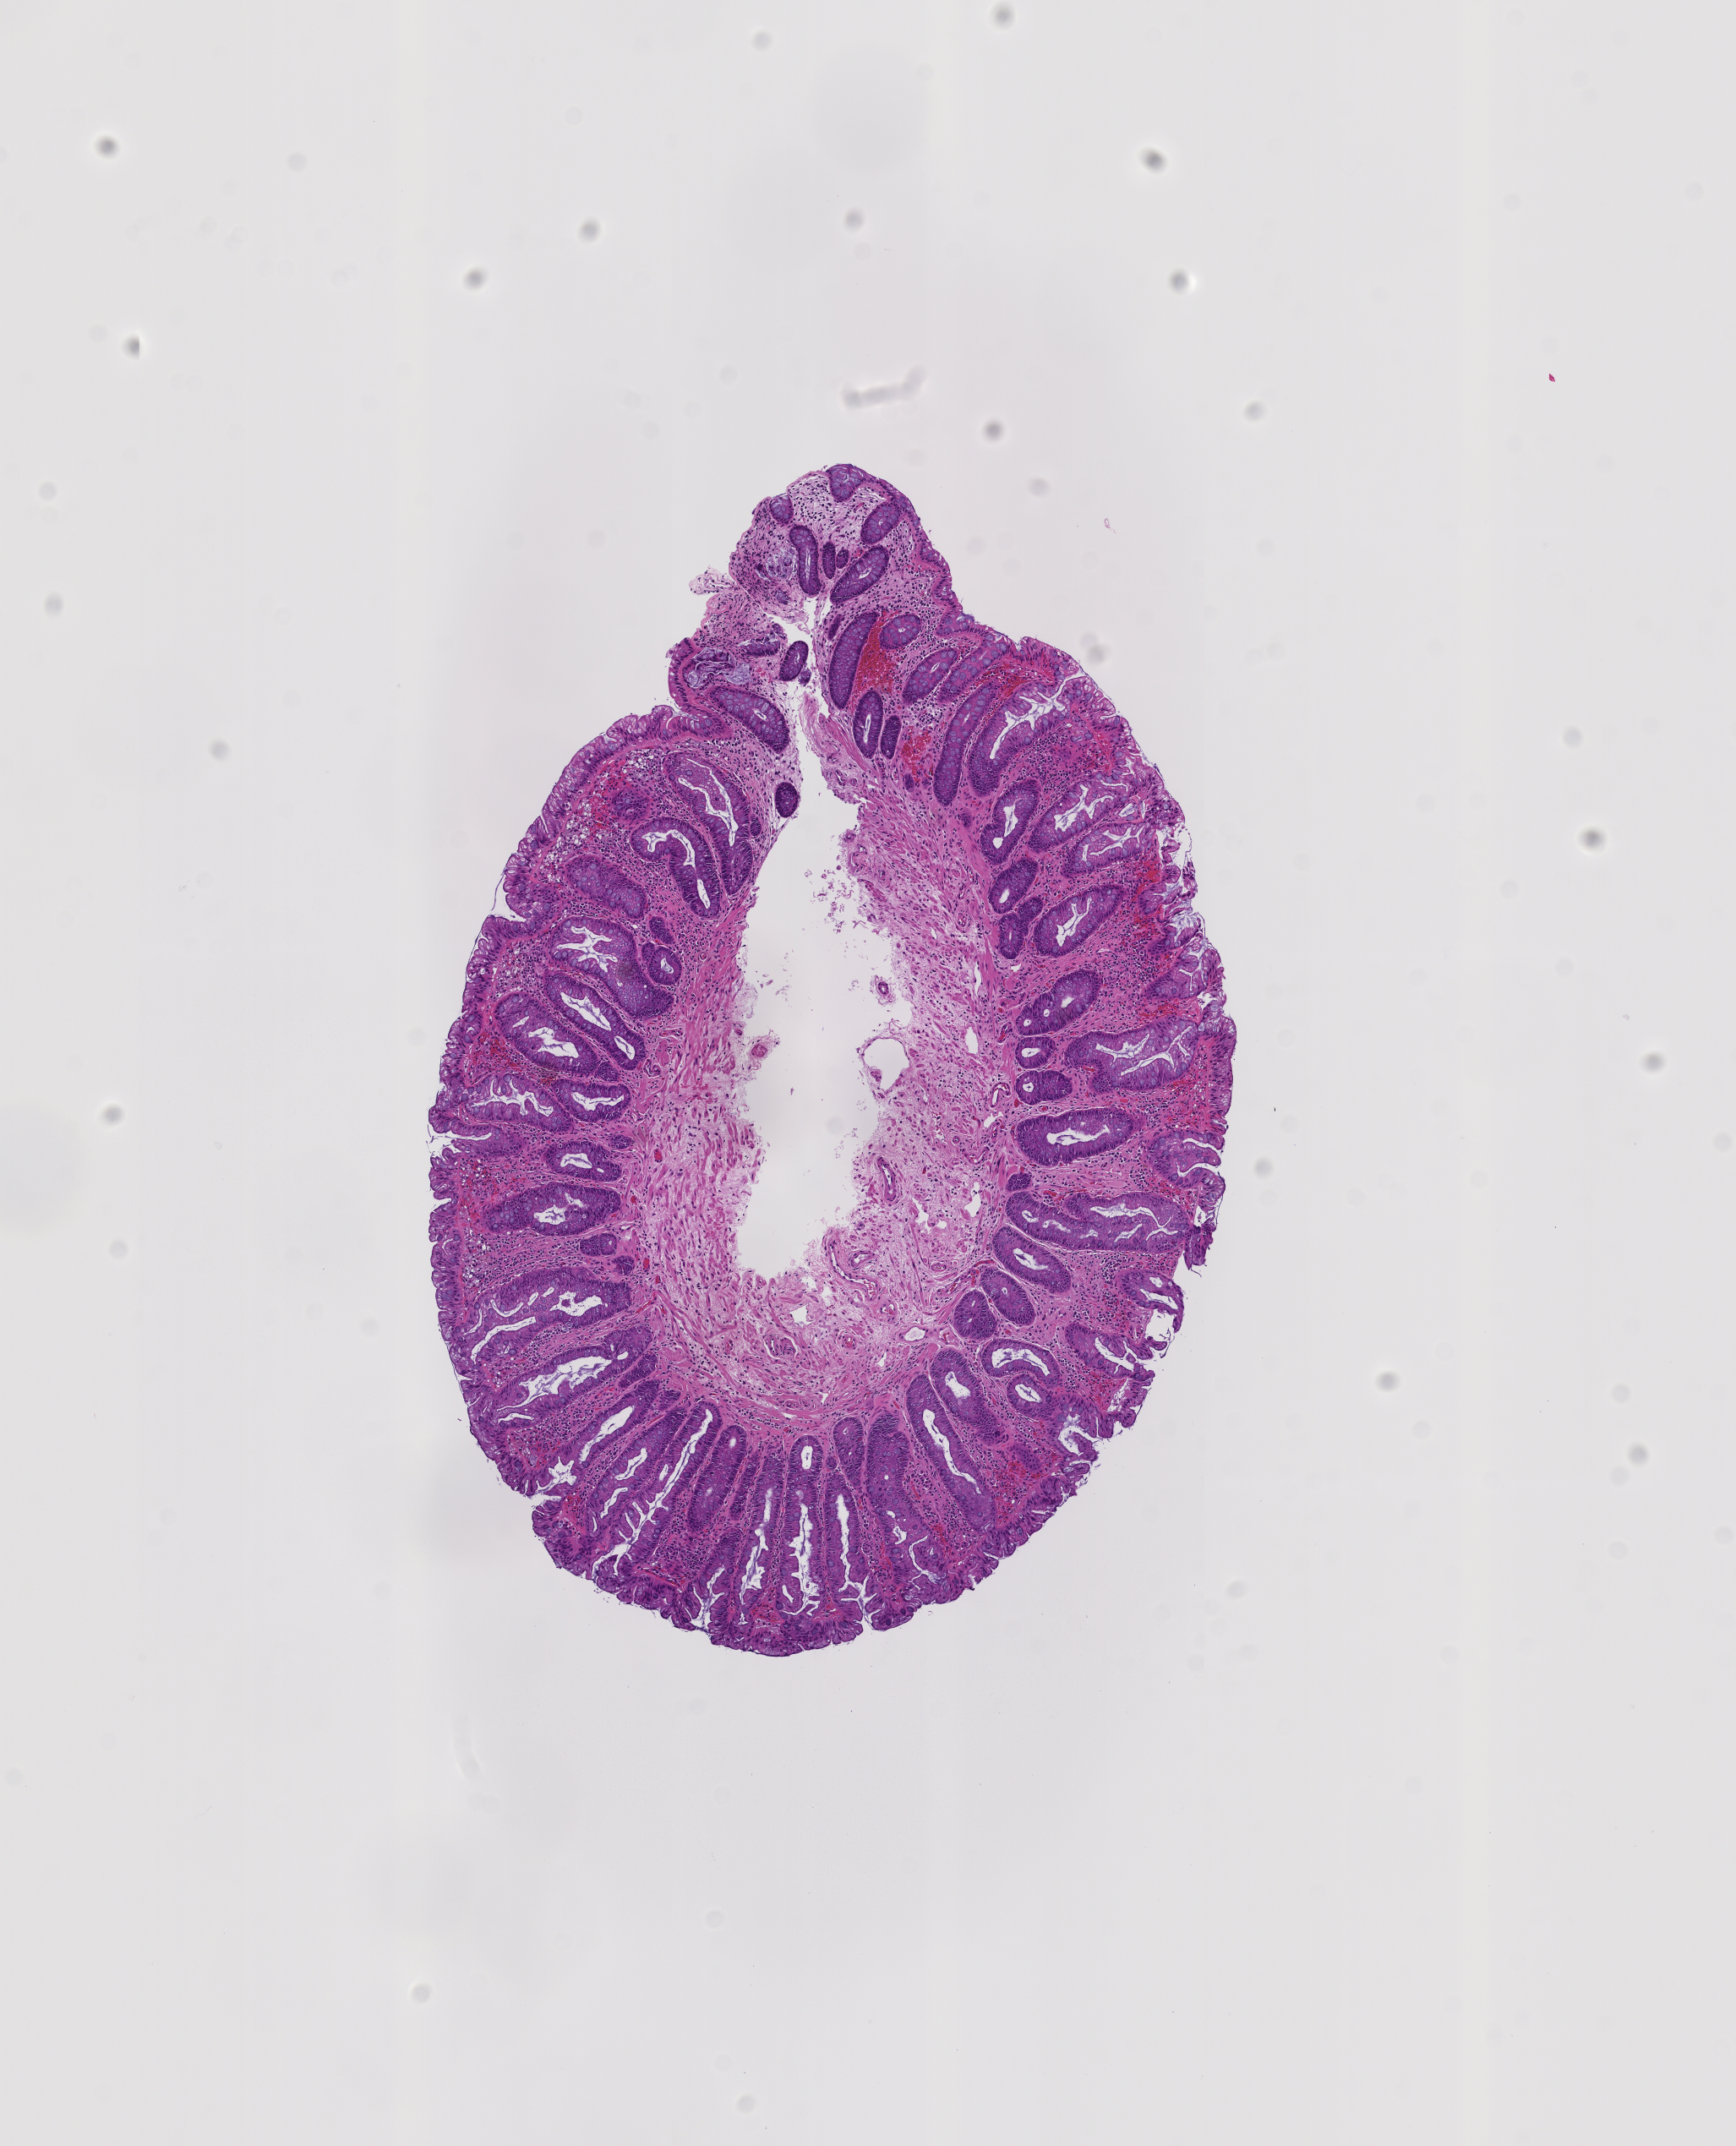
H&E whole-slide image of a colon biopsy, whole scanned area (about 4.1 x 5.1 mm) shown as a low-resolution overview. FFPE section. Site: sigmoid colon. Patient: male.
* lesion category (as recorded): hyperplasia